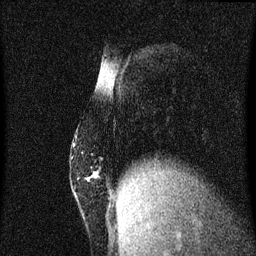
Breast MRI (dynamic contrast-enhanced), one sagittal slice; slice 14 of 60 in the series (ordered by position); dynamic contrast-enhanced series, image 2 of 3 at this slice position (ordered by acquisition); 1.5 T; TE 4.2 ms, TR 8.4 ms; 2 mm slice thickness; 256 × 256 image matrix. Female patient, age 52 years. Case-level facts recorded for this patient, not image findings: setting: breast cancer imaged before/during neoadjuvant chemotherapy; receptor status: HER2-positive.
Outlined on this slice (semi-automatic segmentation, software-assisted and operator-edited):
- analysis volume of interest (the breast-tissue region the enhancement analysis was run in; not a lesion): bounding box [x1, y1, x2, y2] px = [71, 126, 118, 191]
- tumour enhancement mask (voxels above the 70 % enhancement threshold inside the analysis volume of interest): [94, 174, 97, 177]